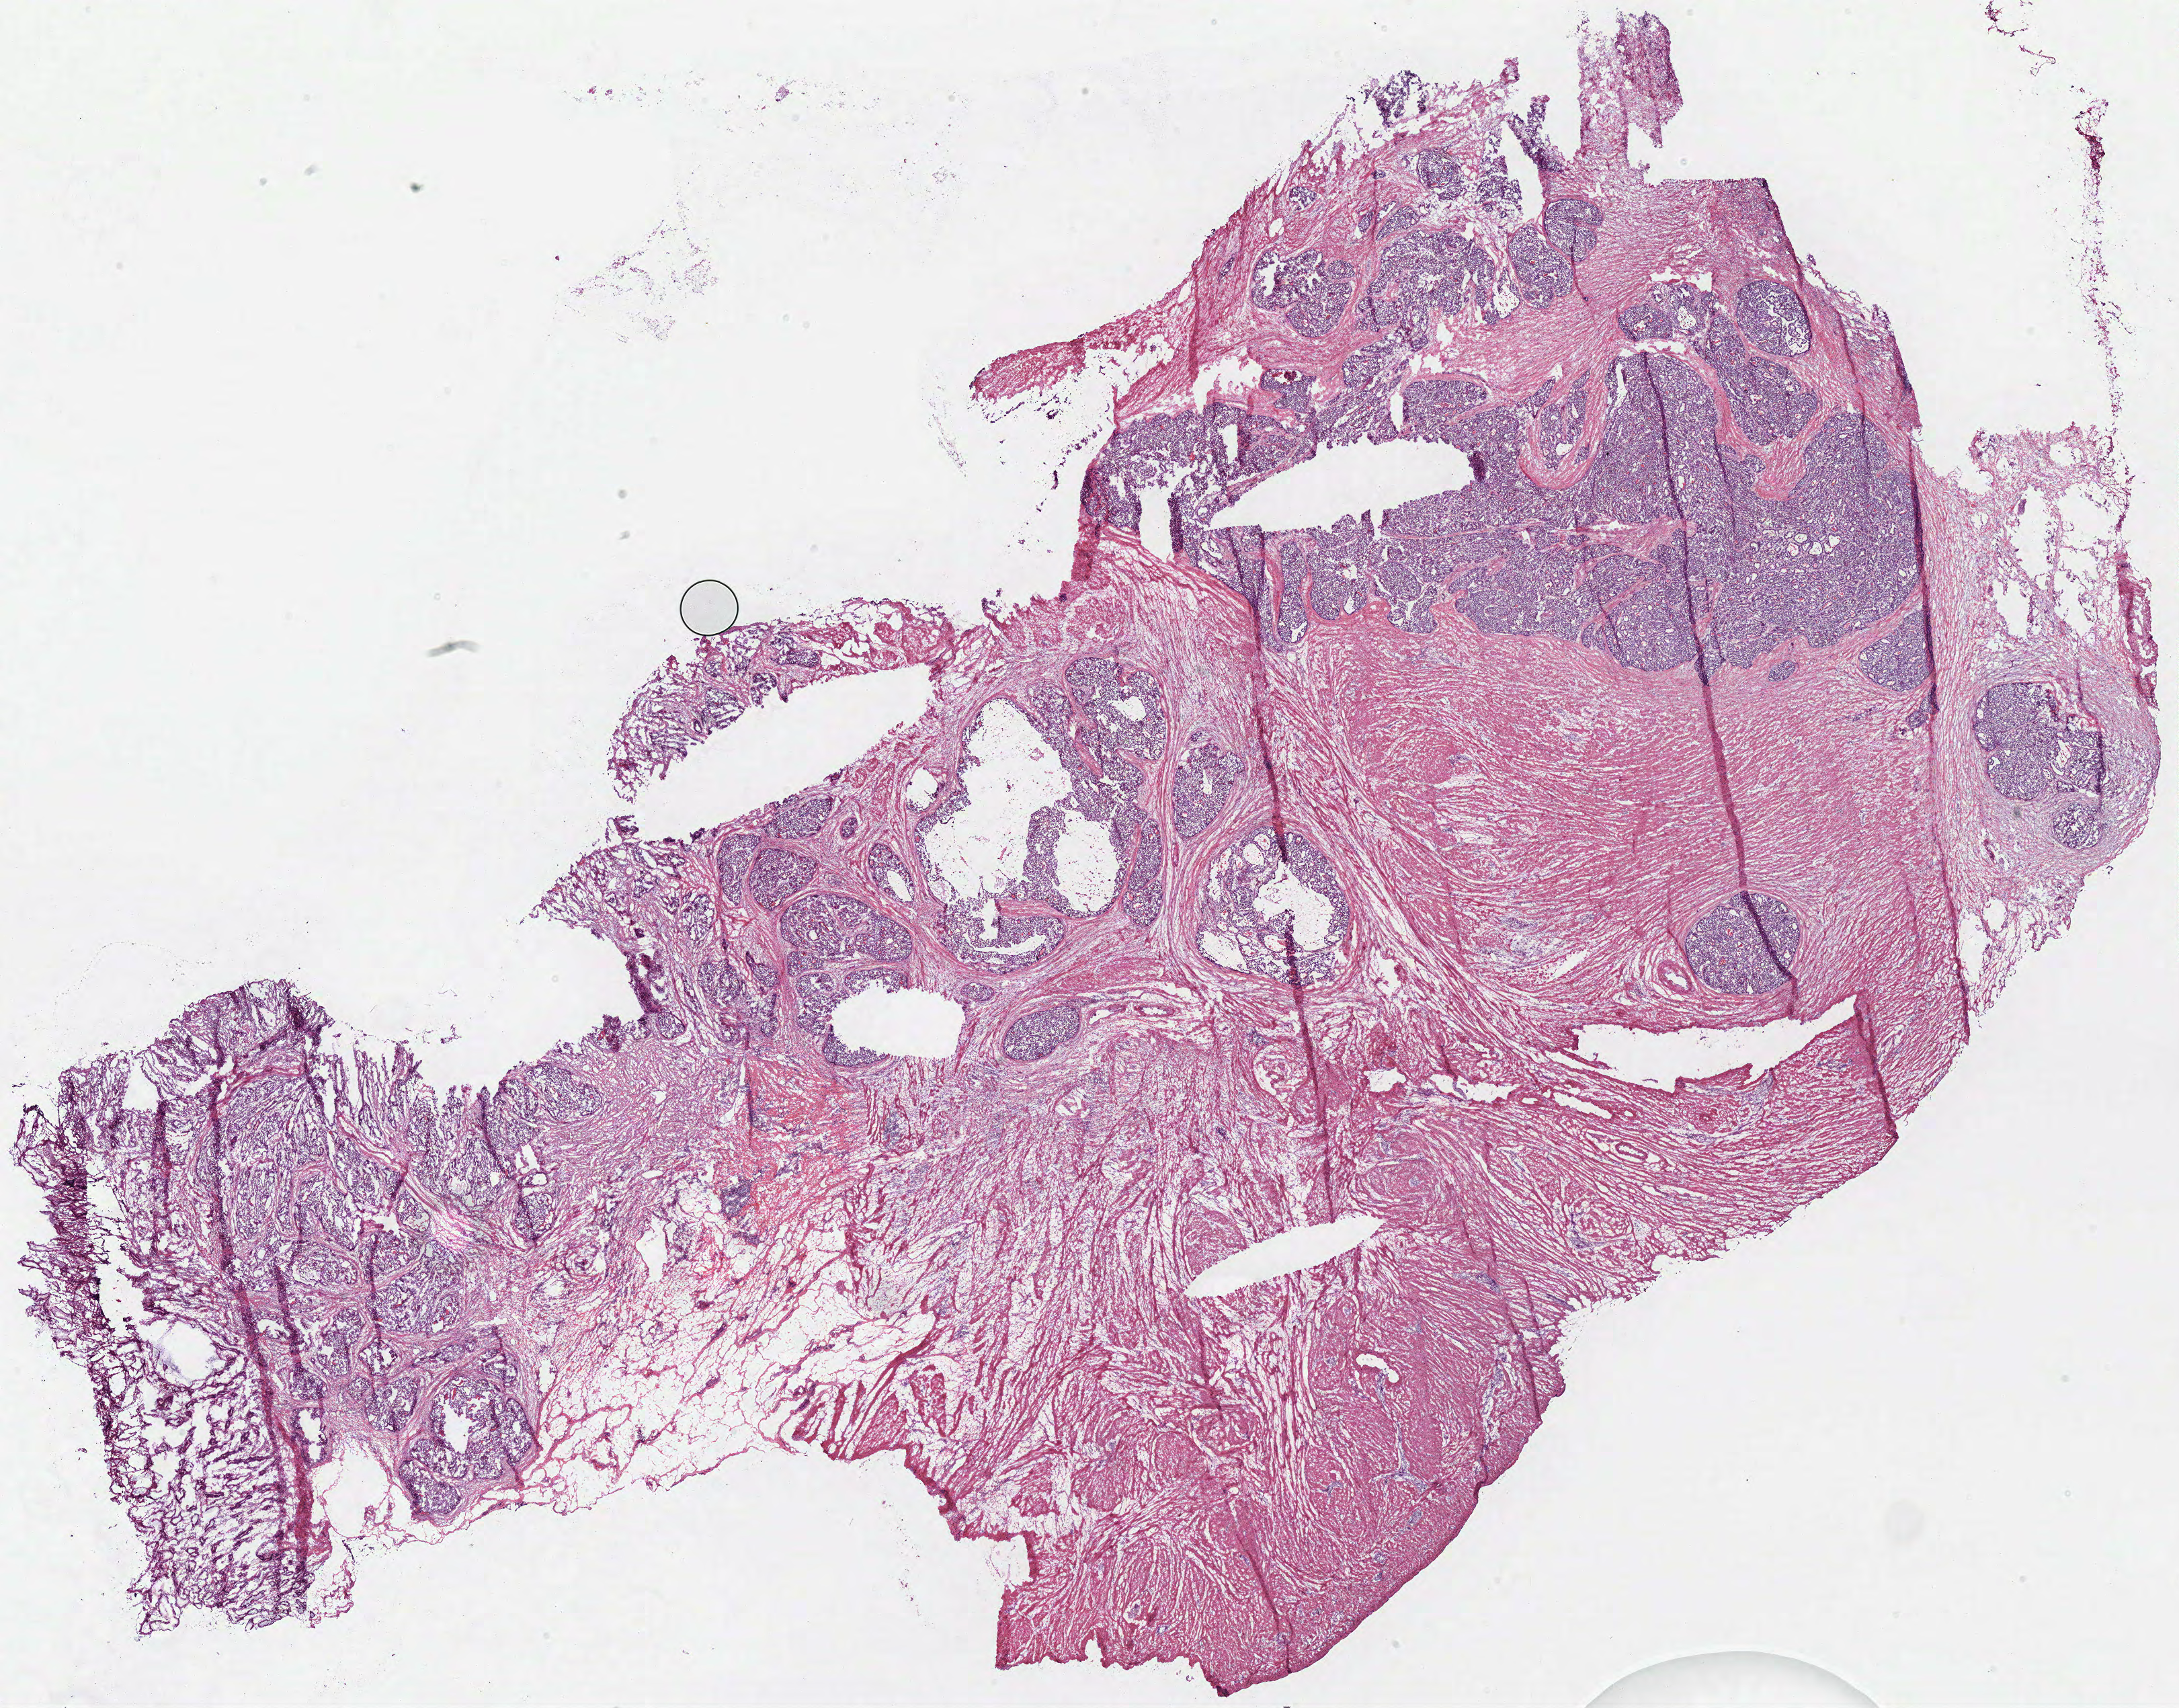
Whole-slide histology image, H&E-stained, whole scanned area (about 25.5 x 20.0 mm, slide scanned at 40x) shown as a low-resolution overview. Frozen section from the bottom of the tissue portion. Primary tumour sample from the stomach. Male, age 69 years at initial diagnosis. Histologic grade: GX (grade cannot be assessed). Slide review estimates, as recorded: tumour cells 45%, tumour nuclei 70%, normal cells 56%, stromal cells 0%, necrosis 4%. Infiltration values recorded for this section: lymphocyte infiltration 10%, monocyte infiltration 0%, neutrophil infiltration 0%.
Lymph nodes positive (case pathology): 0 of 15 examined. AJCC pathologic stage: II. Diagnosis: Adenocarcinoma, NOS (gastric antrum).